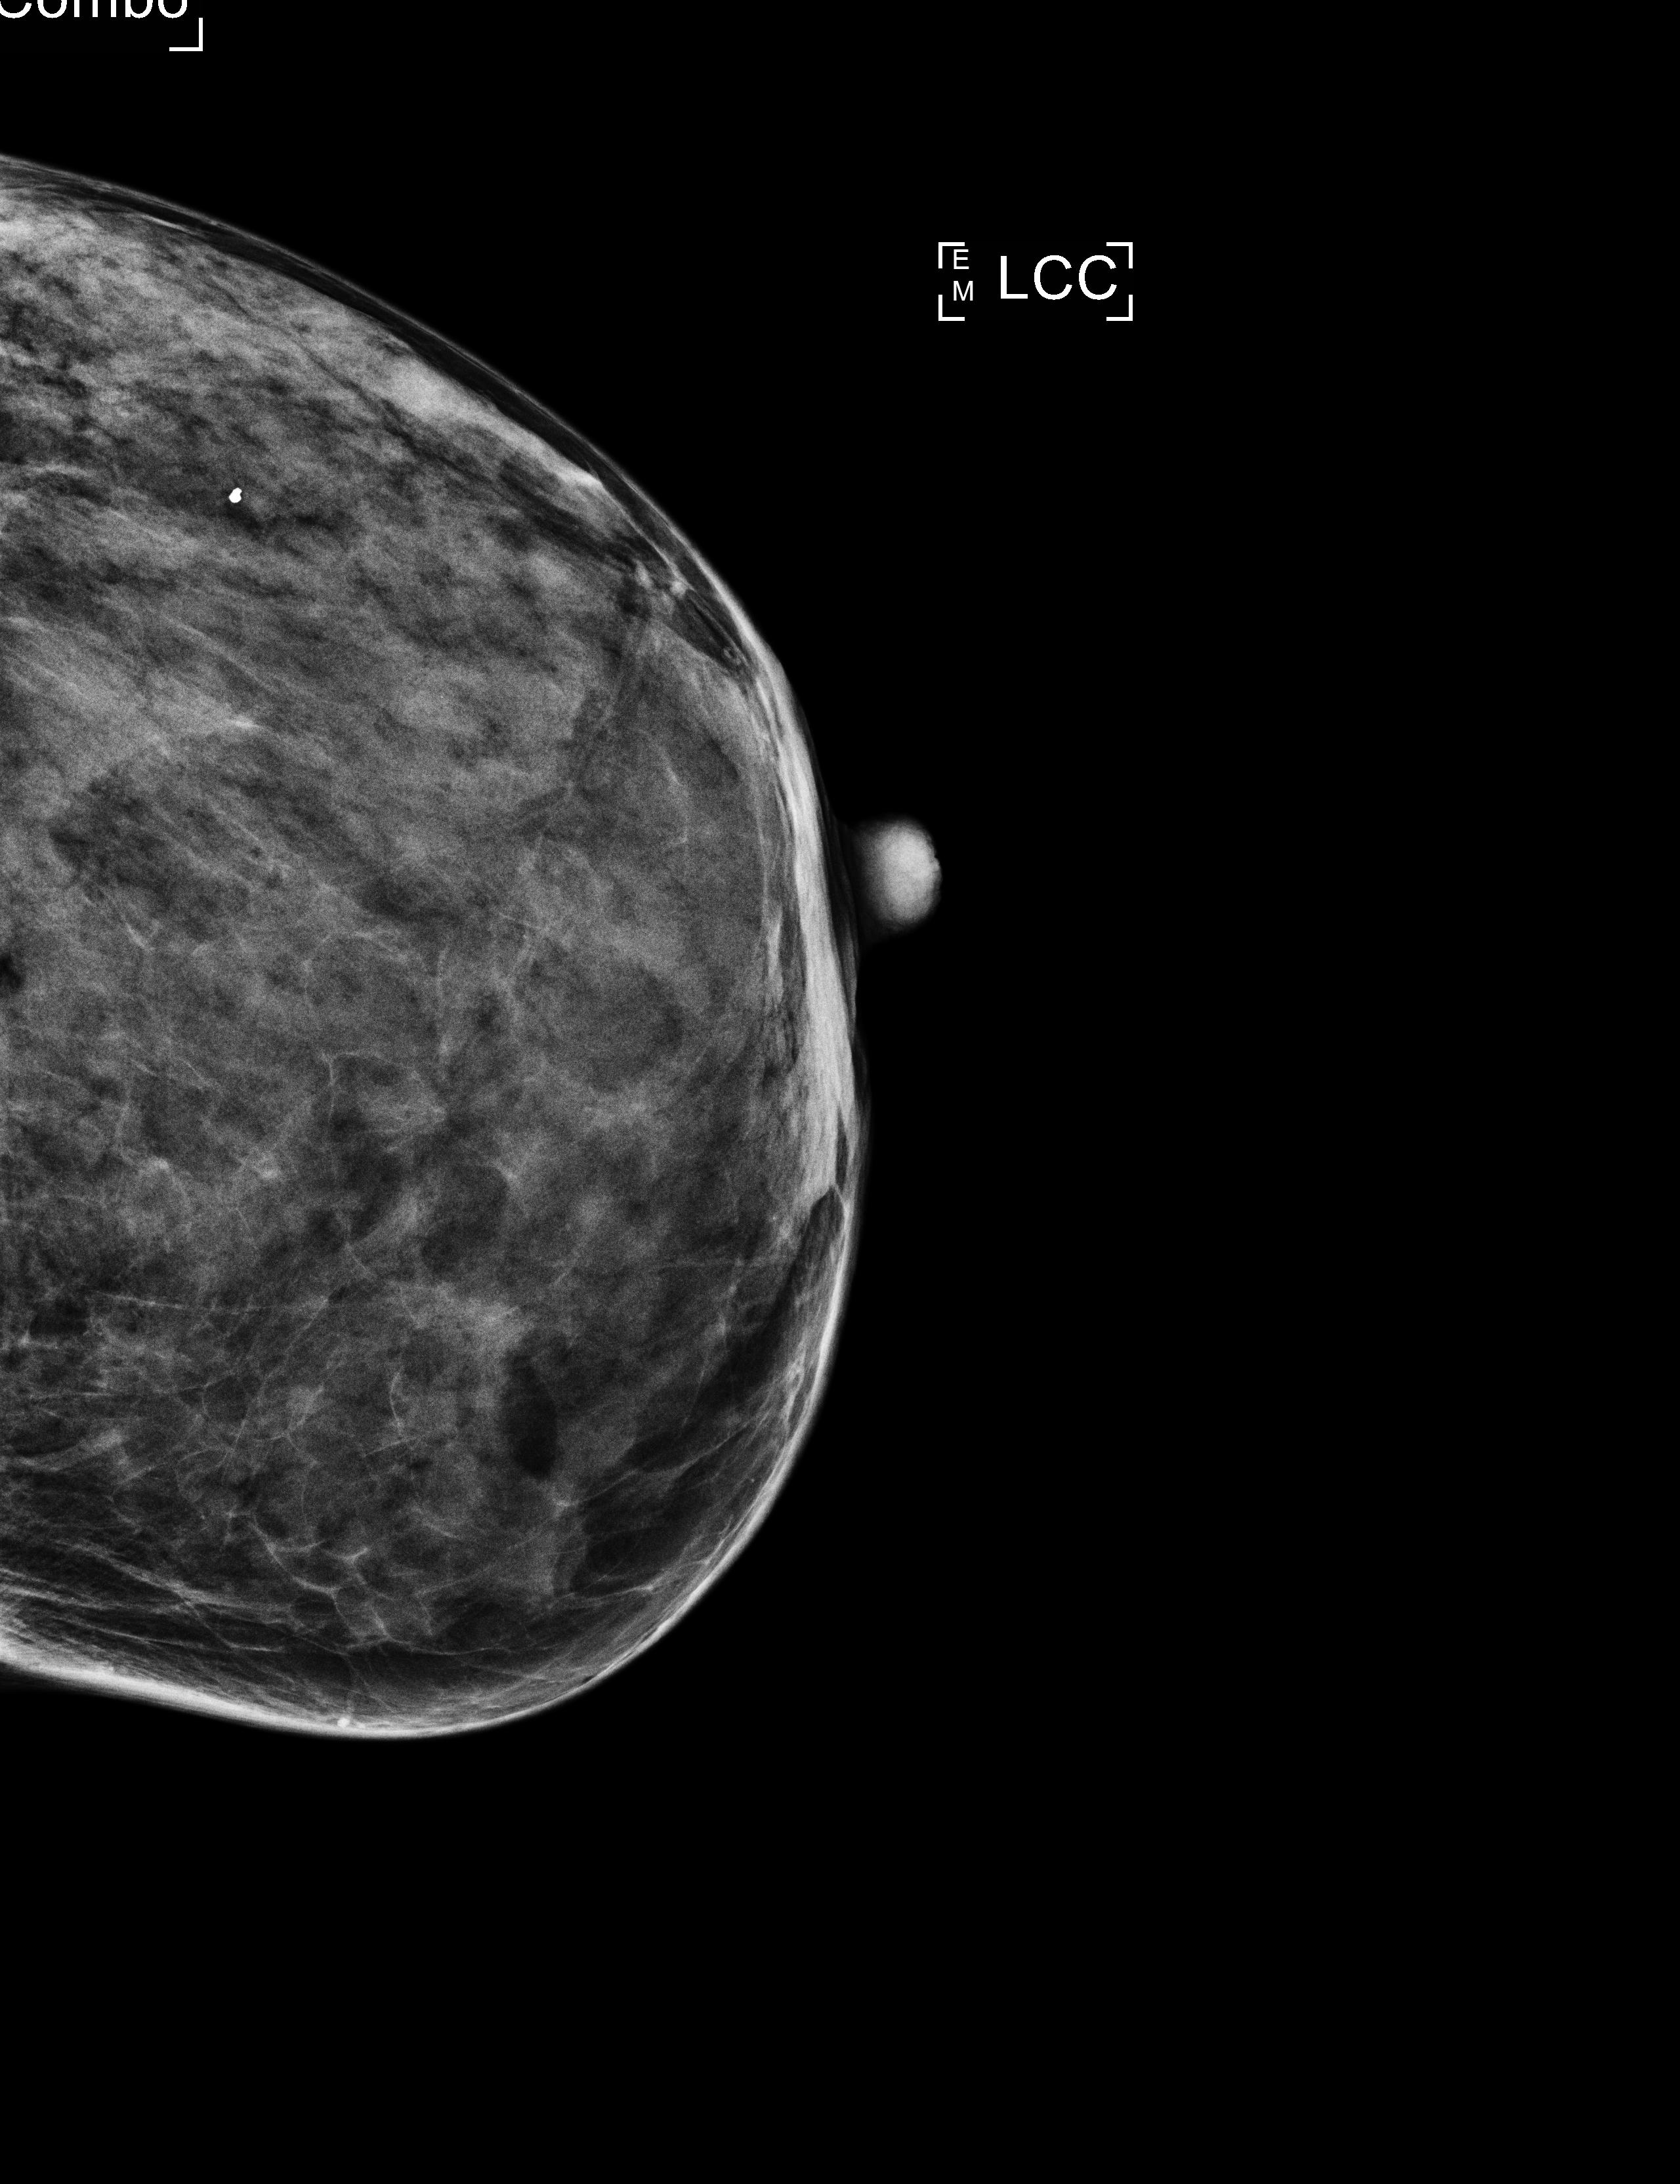
Screening examination; compressed breast thickness 28 mm; system: Selenia Dimensions. Patient: female, 55 years.
Image type: full-field digital mammogram. Breast: left. Projection: CC view. BI-RADS breast density category at the screening exam (both breasts, scale 1–4): 4. Final BI-RADS assessment for this screening round (tomosynthesis exam, both breasts): category 2. Recall: no recall after this screen.